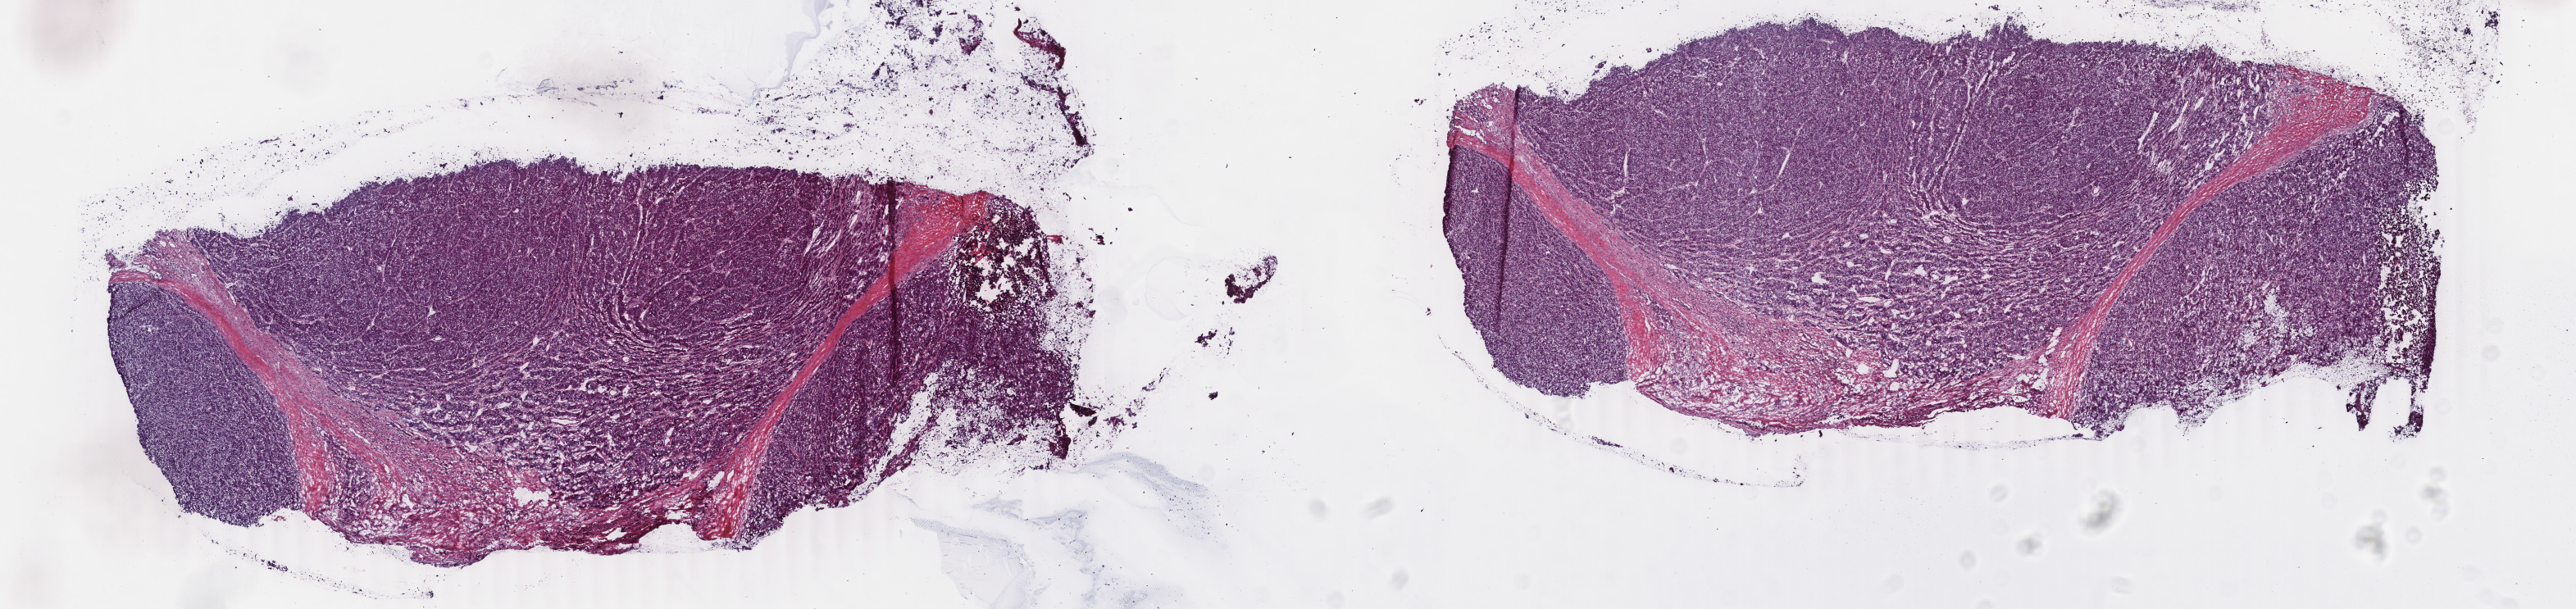
Whole-slide histology image, H&E-stained, low-resolution overview of the scanned area, about 25.0 x 5.9 mm (from a 40x scan), frozen section from the bottom of the tissue portion, primary tumour sample from the liver. Male, age 53 years at initial diagnosis. Histologic grade: G2 (moderately differentiated). Composition of this section per pathologist review: tumour cells 90%, tumour nuclei 90%, normal cells 3%, stromal cells 7%, necrosis 0%. Infiltration values recorded for this section: lymphocyte infiltration 1%, monocyte infiltration 0%, neutrophil infiltration 0%.
AJCC pathologic stage: IIIA (5th edition). Pathologic diagnosis: Hepatocellular carcinoma, NOS.